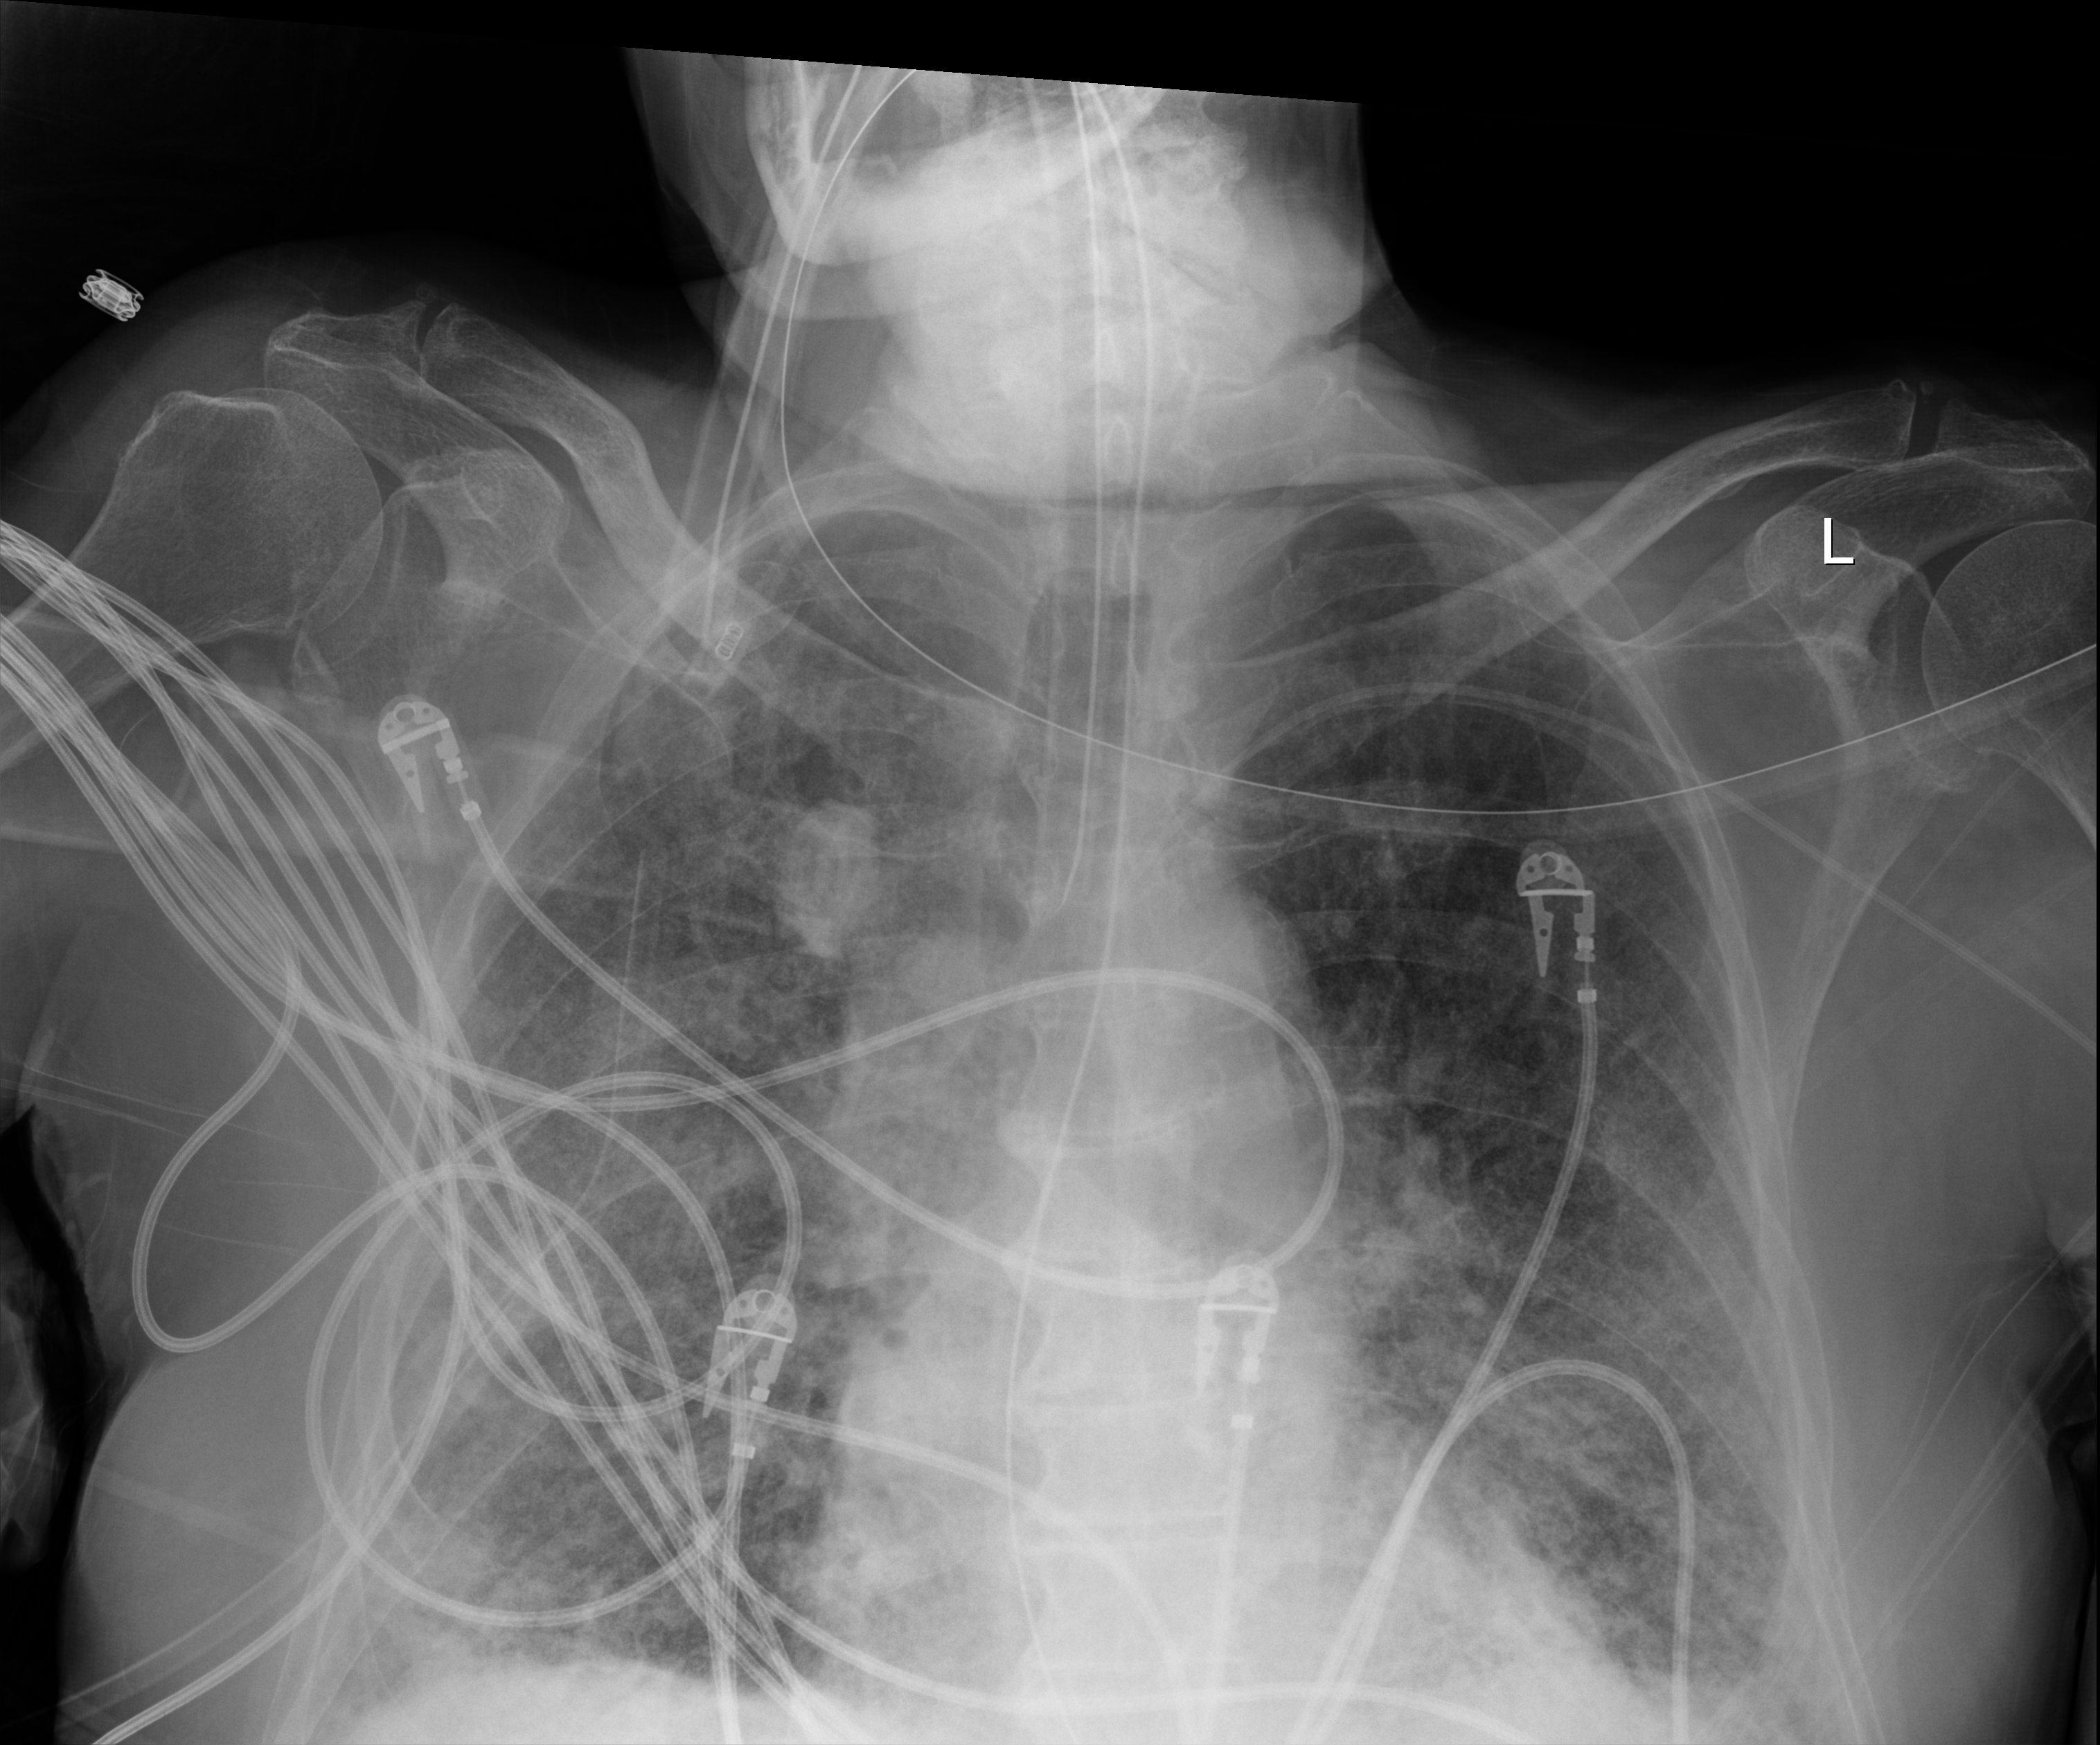
Portable chest radiograph; anteroposterior (AP) projection. Male patient hospitalised with COVID-19, age 75–90 years.
Admission-level facts for this patient (not findings on this image; timing relative to this image not recorded): other chronic lung disease (admission record): no; mechanically ventilated during this hospital stay: yes; hypertension (admission record): no.